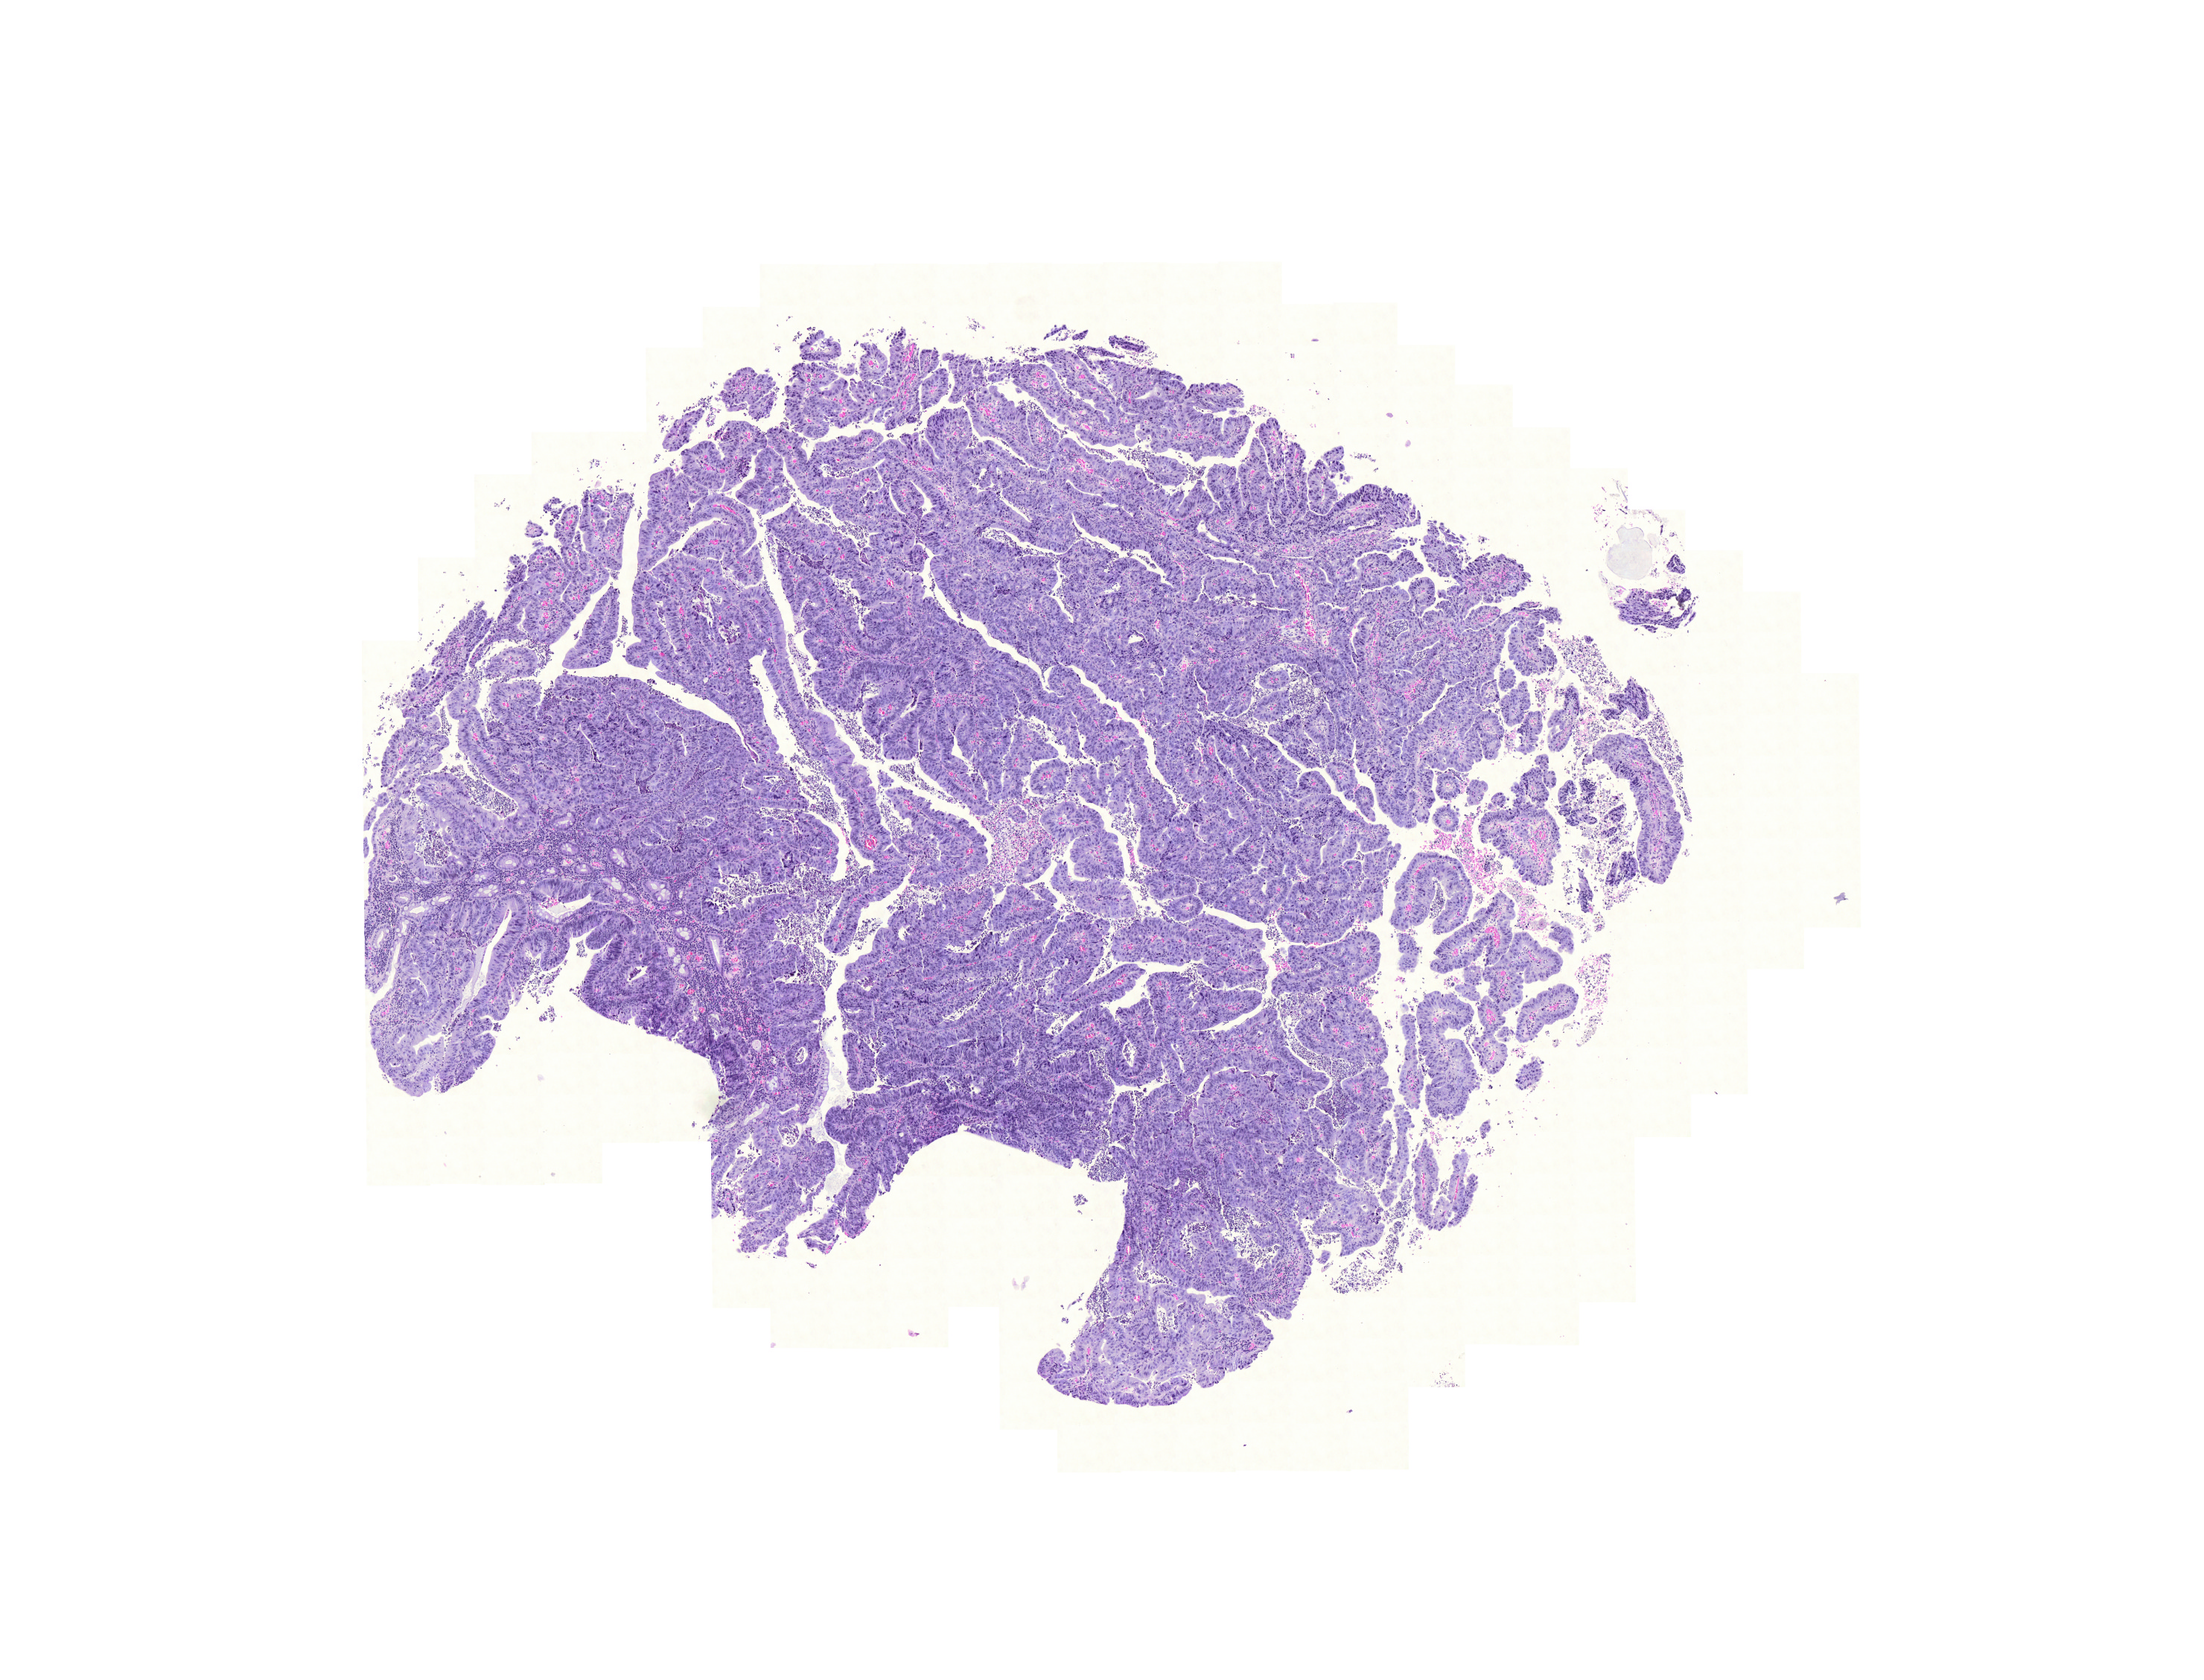
H&E whole-slide image, a low-resolution overview of the entire scanned area, about 11.0 x 8.4 mm; formalin-fixed paraffin-embedded (FFPE) diagnostic section; rectum, primary tumour sample. Male, age 86 years at initial diagnosis.
* pathologic diagnosis: Adenocarcinoma, NOS
* lymph nodes positive (case pathology): 0 of 15 examined
* AJCC pathologic stage: I
* TNM: T2 N0 M0